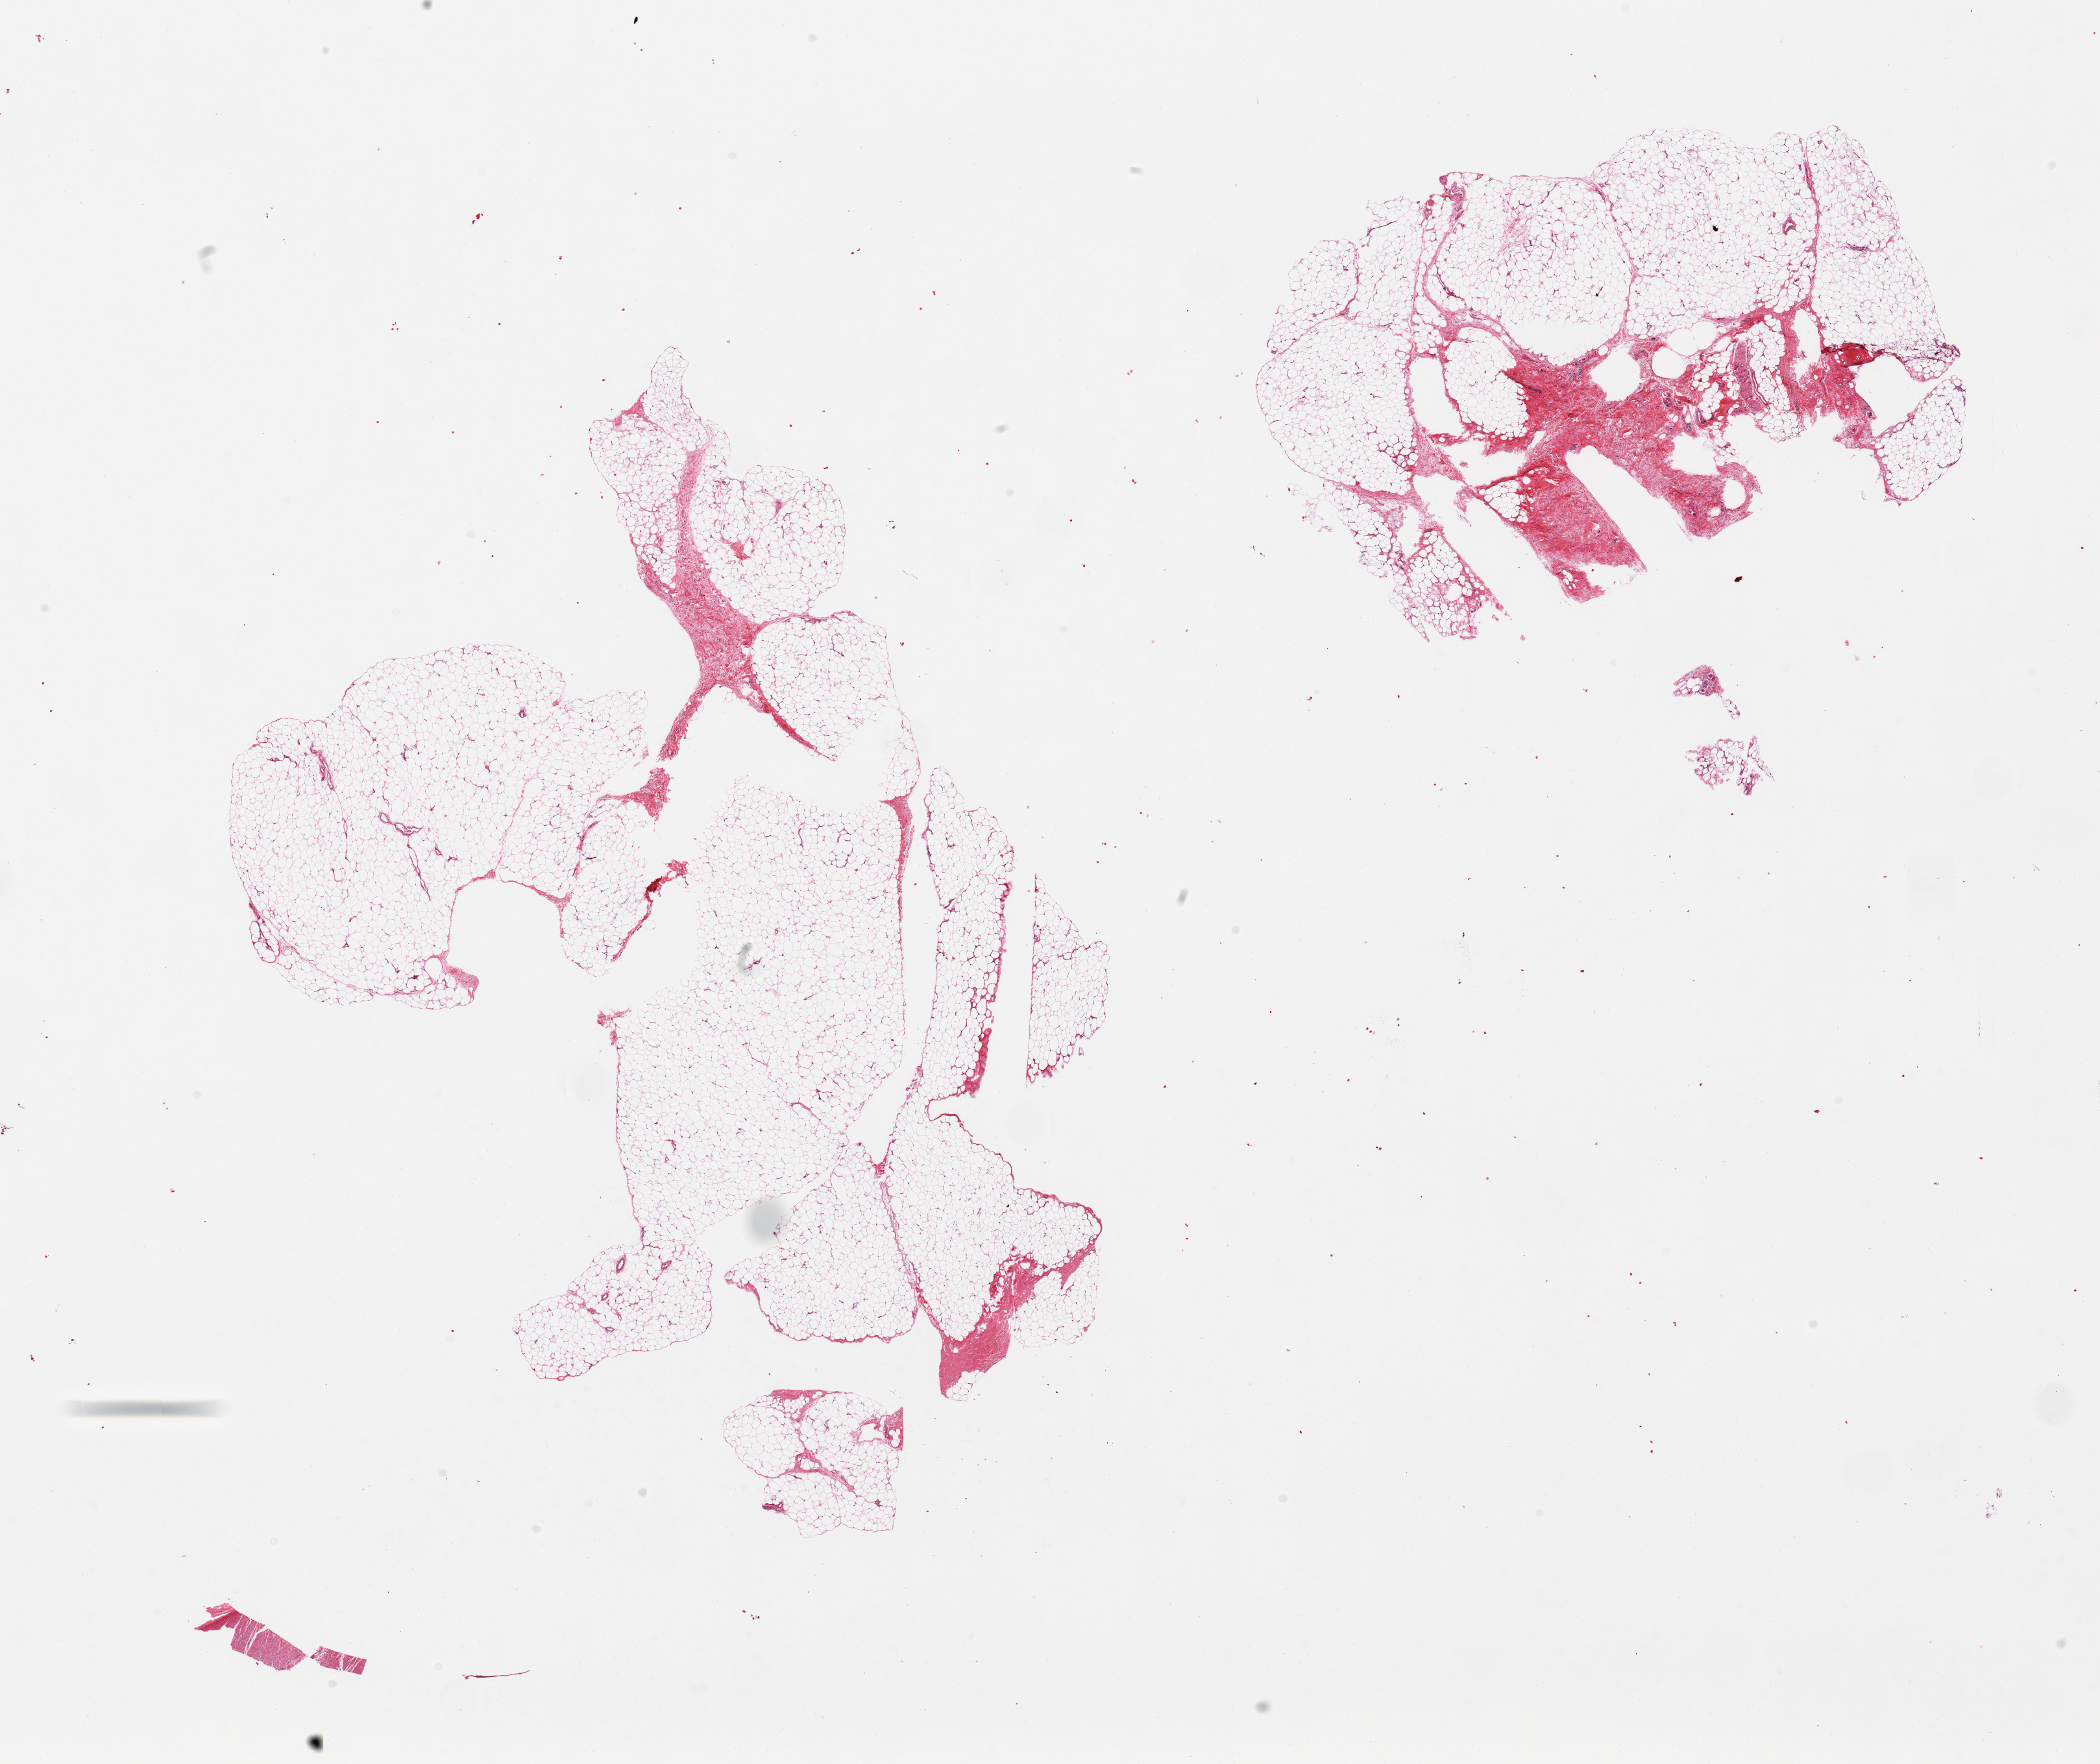
Digitized hematoxylin and eosin (H&E)-stained section, brightfield, whole scanned area (about 25.6 x 21.5 mm, from a 20x scan) shown as a low-resolution overview; PAXgene-fixed, paraffin-embedded tissue; target tissue: adipose tissue; donor tissue sample.
• reviewer comment on this tissue sample: 2 pieces, scattered giant cell reaction with asteroid bodies within fibrous component